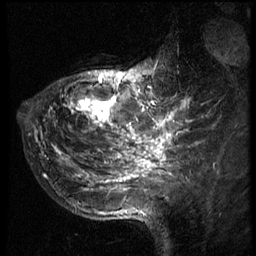
Breast MRI (dynamic contrast-enhanced), one sagittal slice. Position 21 of 66 along the scan axis. 3 images stored at this slice position (order not interpretable as contrast timing). 1.5 T. TE 4.2 ms, TR 8.9 ms. 256 × 256 image matrix, field of view 200 × 200 mm. Patient: female, 39 years. From the clinical record (not read from this slice): setting: breast cancer imaged before/during neoadjuvant chemotherapy; receptor status: HER2-positive.
Annotated regions visible in this slice (semi-automatic segmentation, software-assisted and operator-edited):
- analysis volume of interest (the breast-tissue region the enhancement analysis was run in; not a lesion): box from (x=29, y=45) to (x=166, y=196) px
- tumour enhancement mask (voxels above the 140 % enhancement threshold inside the analysis volume of interest): (x=35, y=72)–(x=156, y=183)